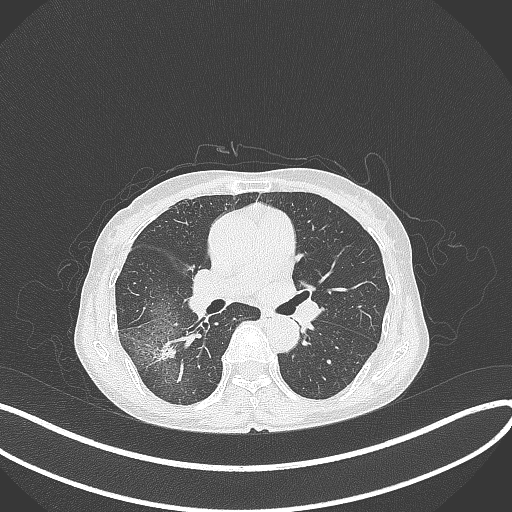
Chest CT, one axial slice; position 220 of 371 along the scan axis; reconstruction kernel B70f; lung window (W 1500 / L -600 HU); 1 mm slice thickness; 512 × 512 image matrix, field of view 400 × 400 mm. Patient: female, 69 years. From the clinical record (not read from this slice): clinical TNM (as recorded): T1b N0 M0.
Structures marked on this image (bounding box drawn by a radiologist):
- lung tumour (recorded histology: adenocarcinoma): bounding box (x1, y1, x2, y2) in pixels: (153, 340, 178, 364)